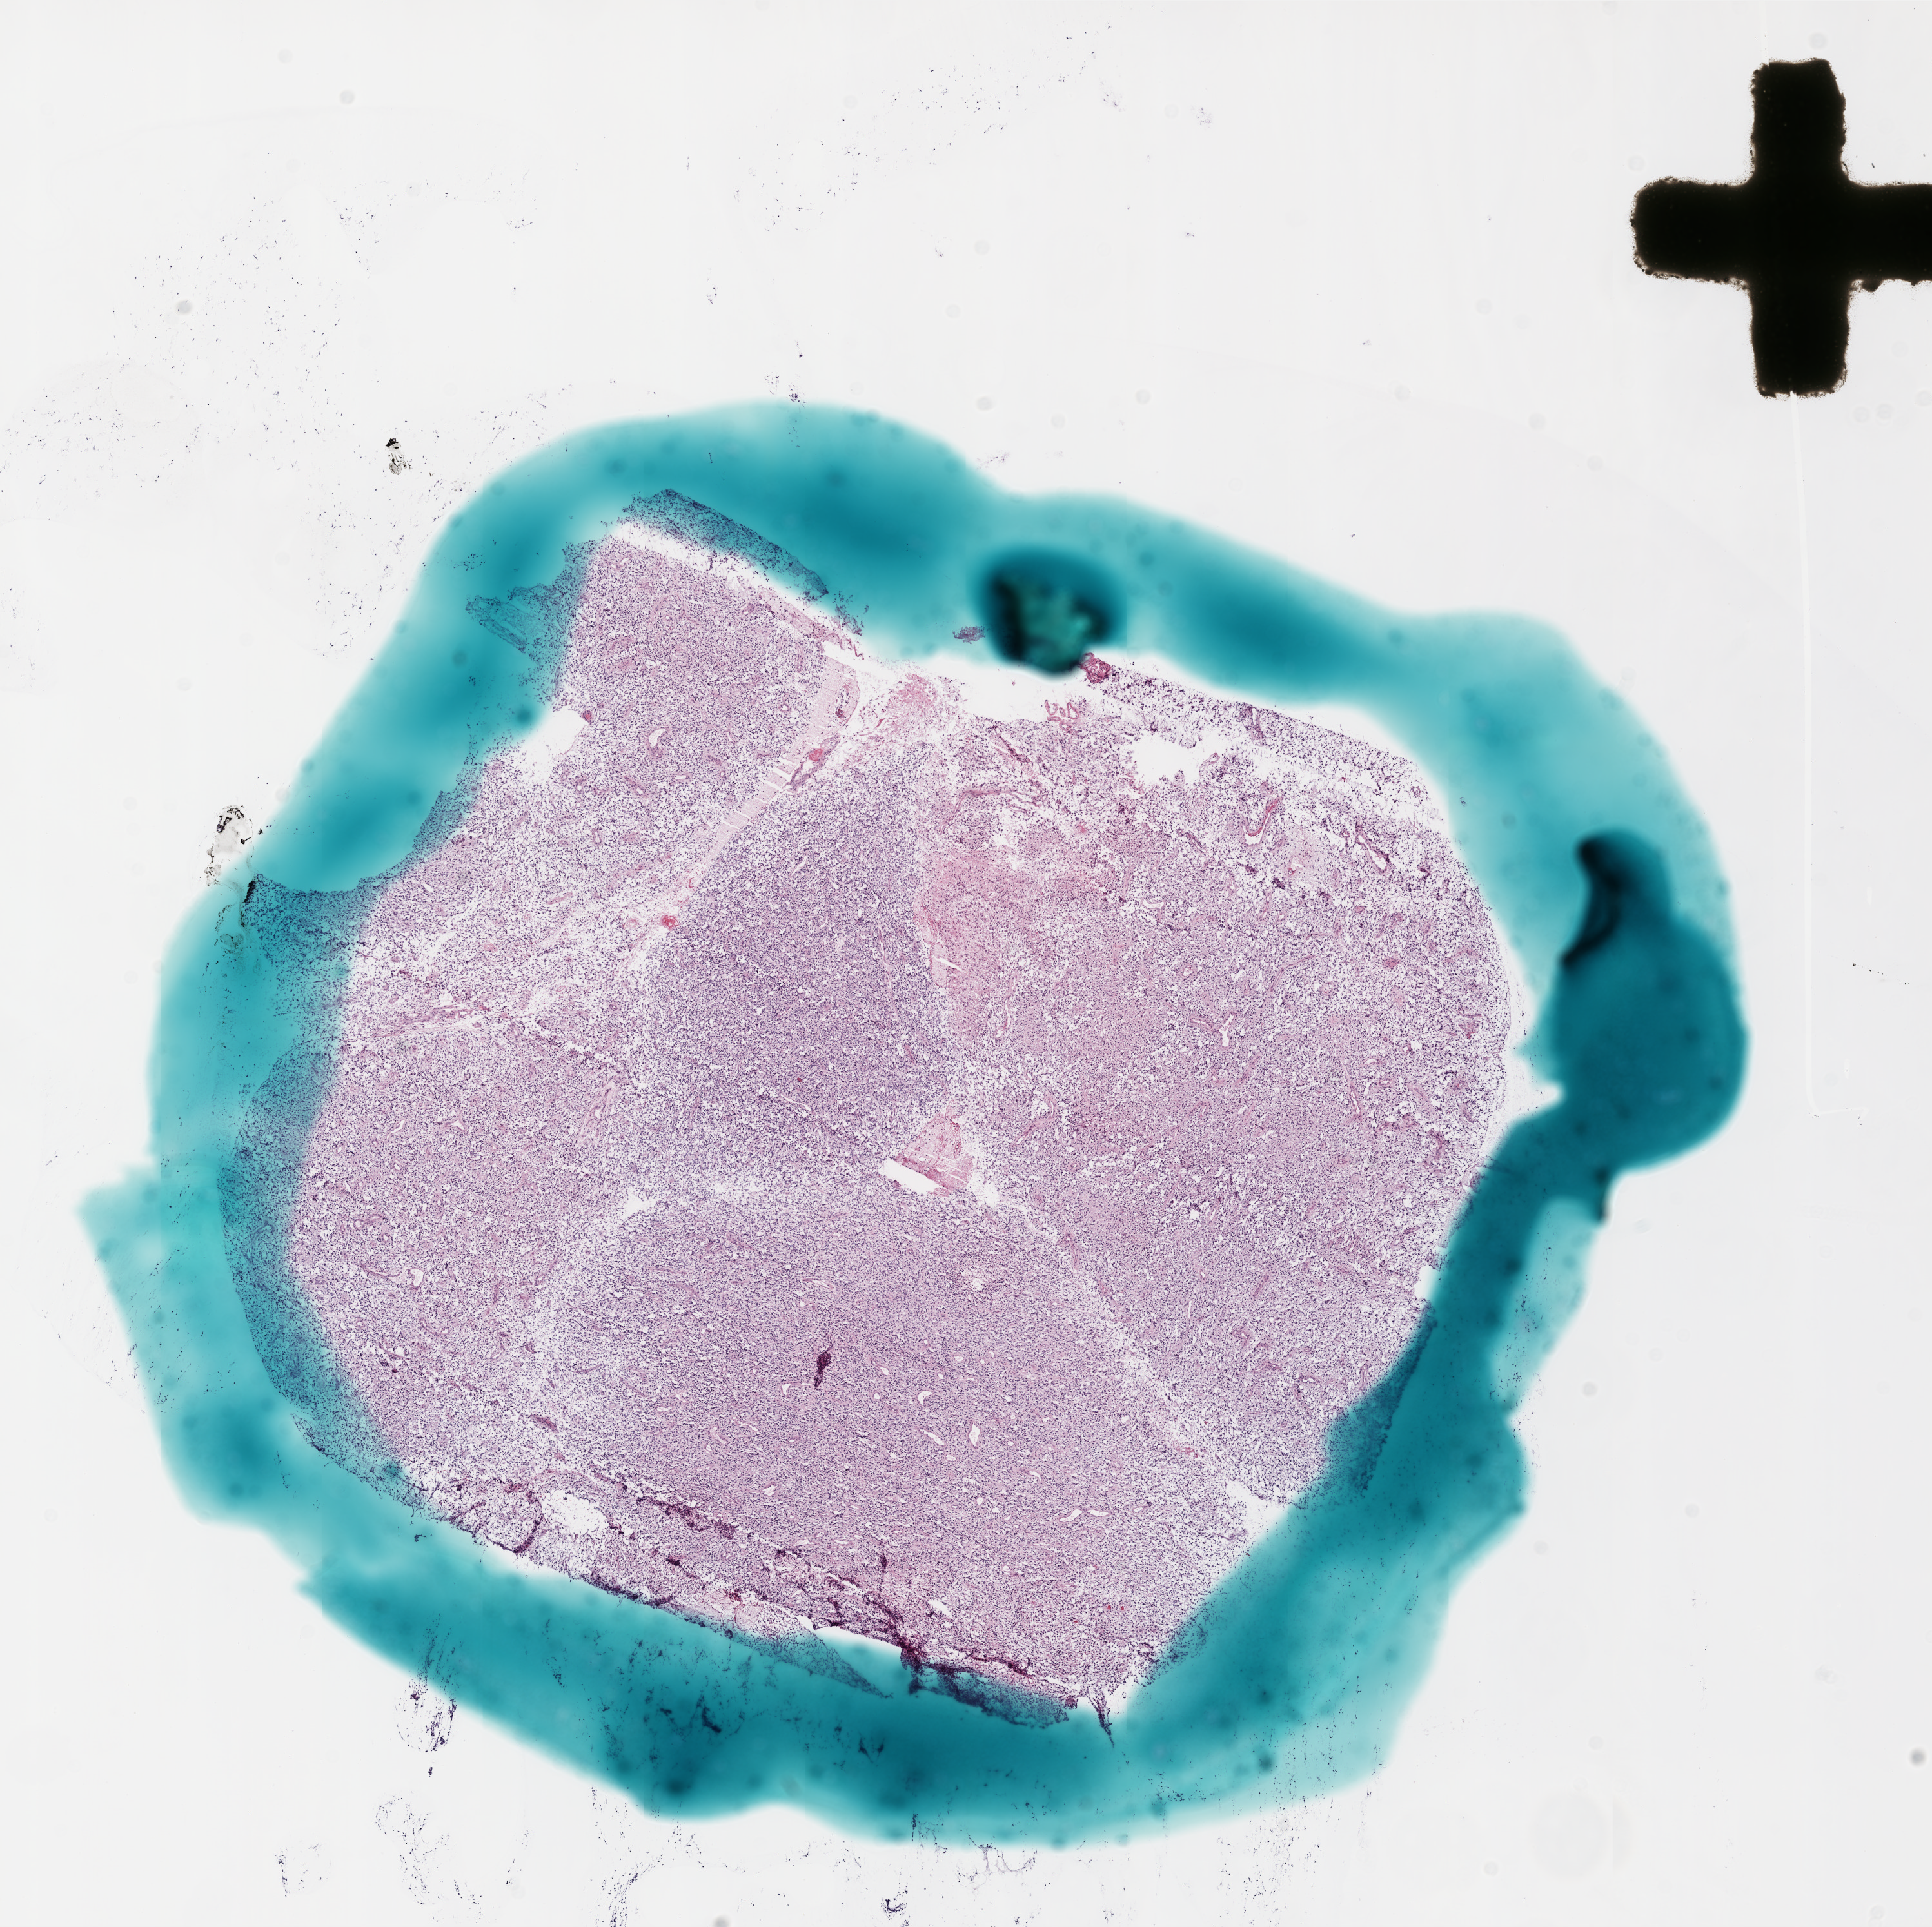
Whole-slide histology image, H&E-stained, whole scanned area (about 12.0 x 12.0 mm, slide scanned at 20x) shown as a low-resolution overview, frozen section from the bottom of the tissue portion, sample: primary tumour, brain. Female, age 63 years at initial diagnosis. Pathologist review of this section (percent, as recorded): tumour cells 95%, tumour nuclei 100%, normal cells 0%, stromal cells 0%, necrosis 5%.
Histologic diagnosis: Glioblastoma.